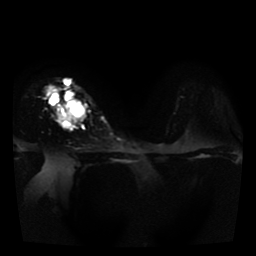
Breast MRI, one axial slice. Slice 28 of 41 in the series (ordered by position). Diffusion-weighted series; image 2 of 4 stored at this slice position (different b-values; order by instance number). 1.5 T. 5 mm slice thickness. 256 × 256 image matrix, field of view 330 × 330 mm. Female patient.
Outlined on this slice (outlined manually by an expert reader):
- tumour on diffusion-weighted imaging: box from (x=58, y=101) to (x=80, y=128) px